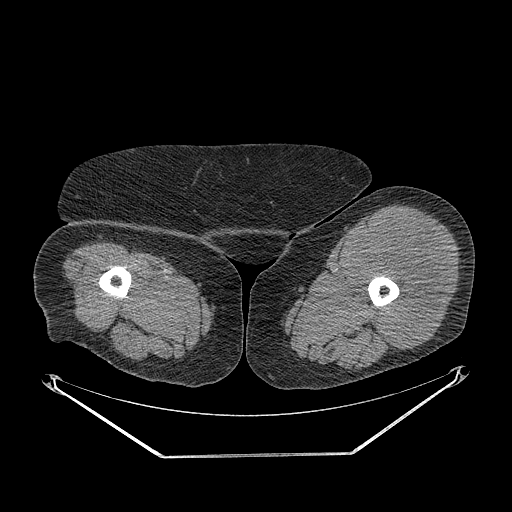
CT of an extremity soft-tissue mass (from a PET/CT study), one axial slice; position 235 of 267 along the scan axis; reconstruction kernel STANDARD; 140 kVp; soft-tissue window (W 400 / L 40 HU); 512 × 512 image matrix. Female patient. Case-level facts recorded for this patient, not image findings: histological type: undifferentiated – high grade; grade: high; site of the primary tumour: left thigh.
Outlined on this slice (expert contour drawn on MRI and transferred to this co-registered scan by the dataset authors):
- gross tumour volume including surrounding oedema: box from (x=352, y=219) to (x=448, y=350) px
- gross tumour volume (mass): (x=352, y=219)–(x=446, y=350)